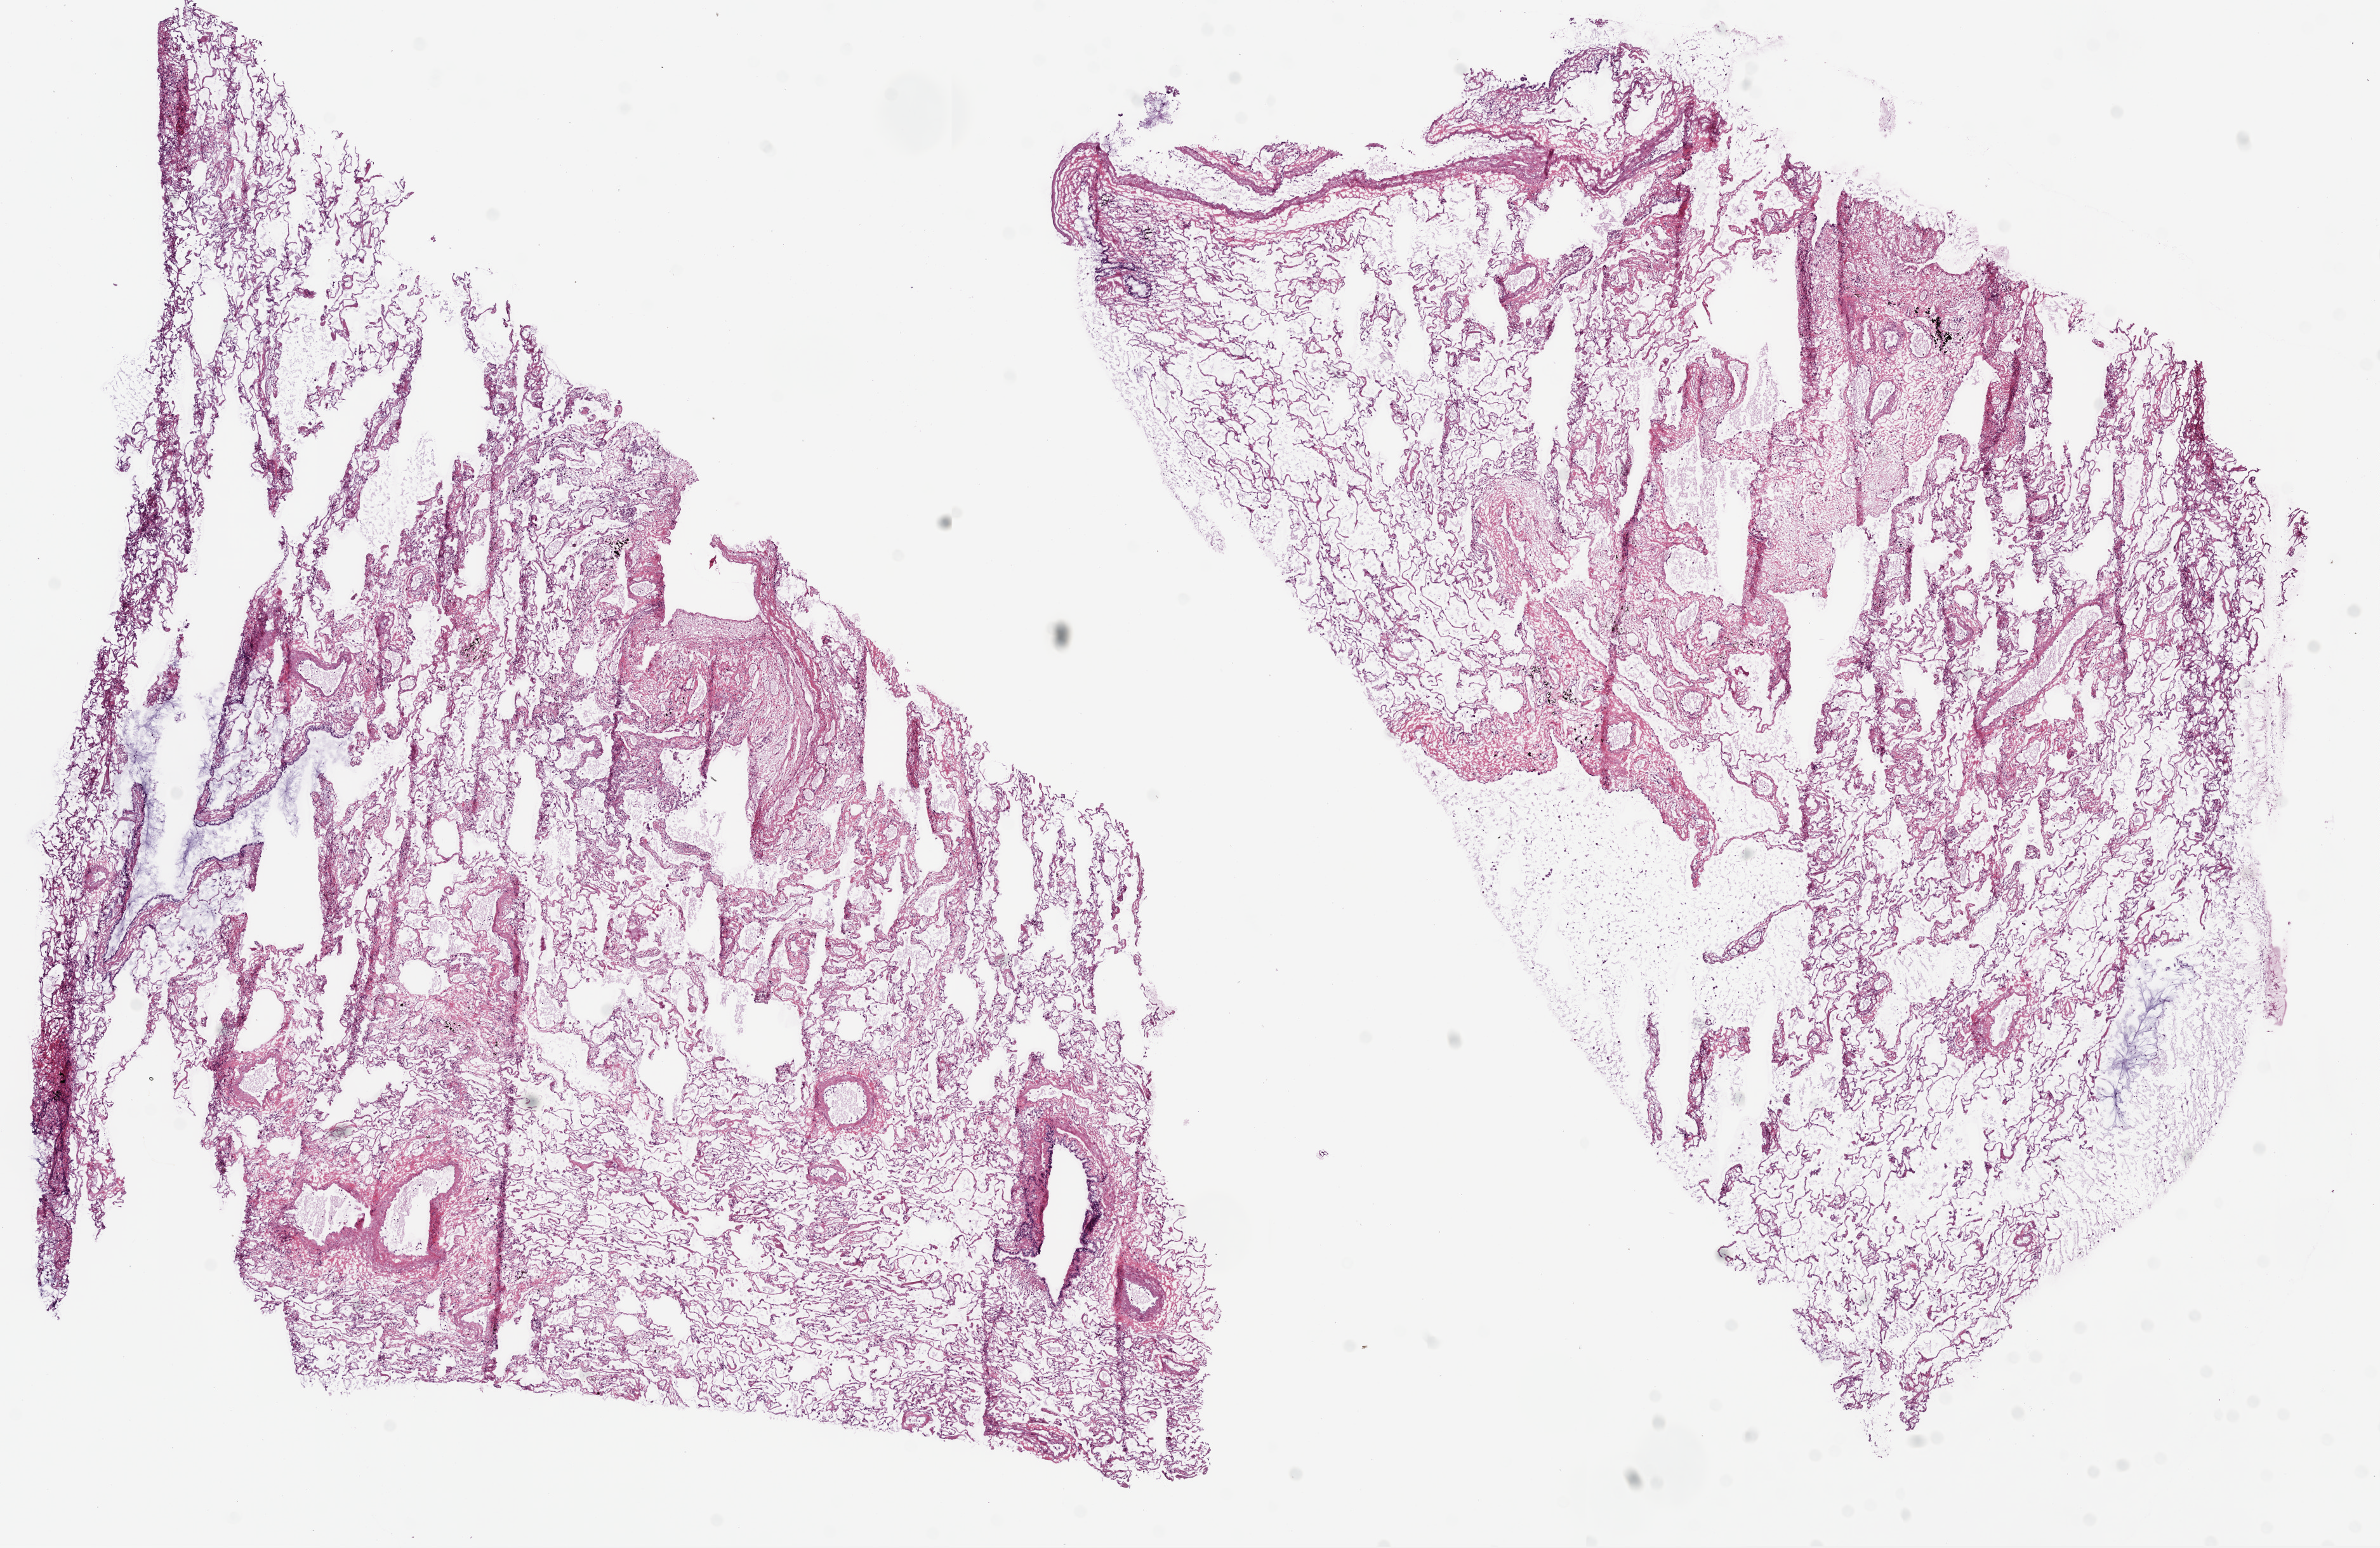
H&E whole-slide image — whole scanned area (about 15.0 x 9.8 mm, acquisition: 20x scan) shown as a low-resolution overview, frozen section, lung, solid tissue normal (non-tumour tissue) sample. Male, age 66 years at initial diagnosis.
This section: solid tissue normal (non-tumour) sample from the same patient. Patient diagnosis: Squamous cell carcinoma, NOS (upper lobe, lung).